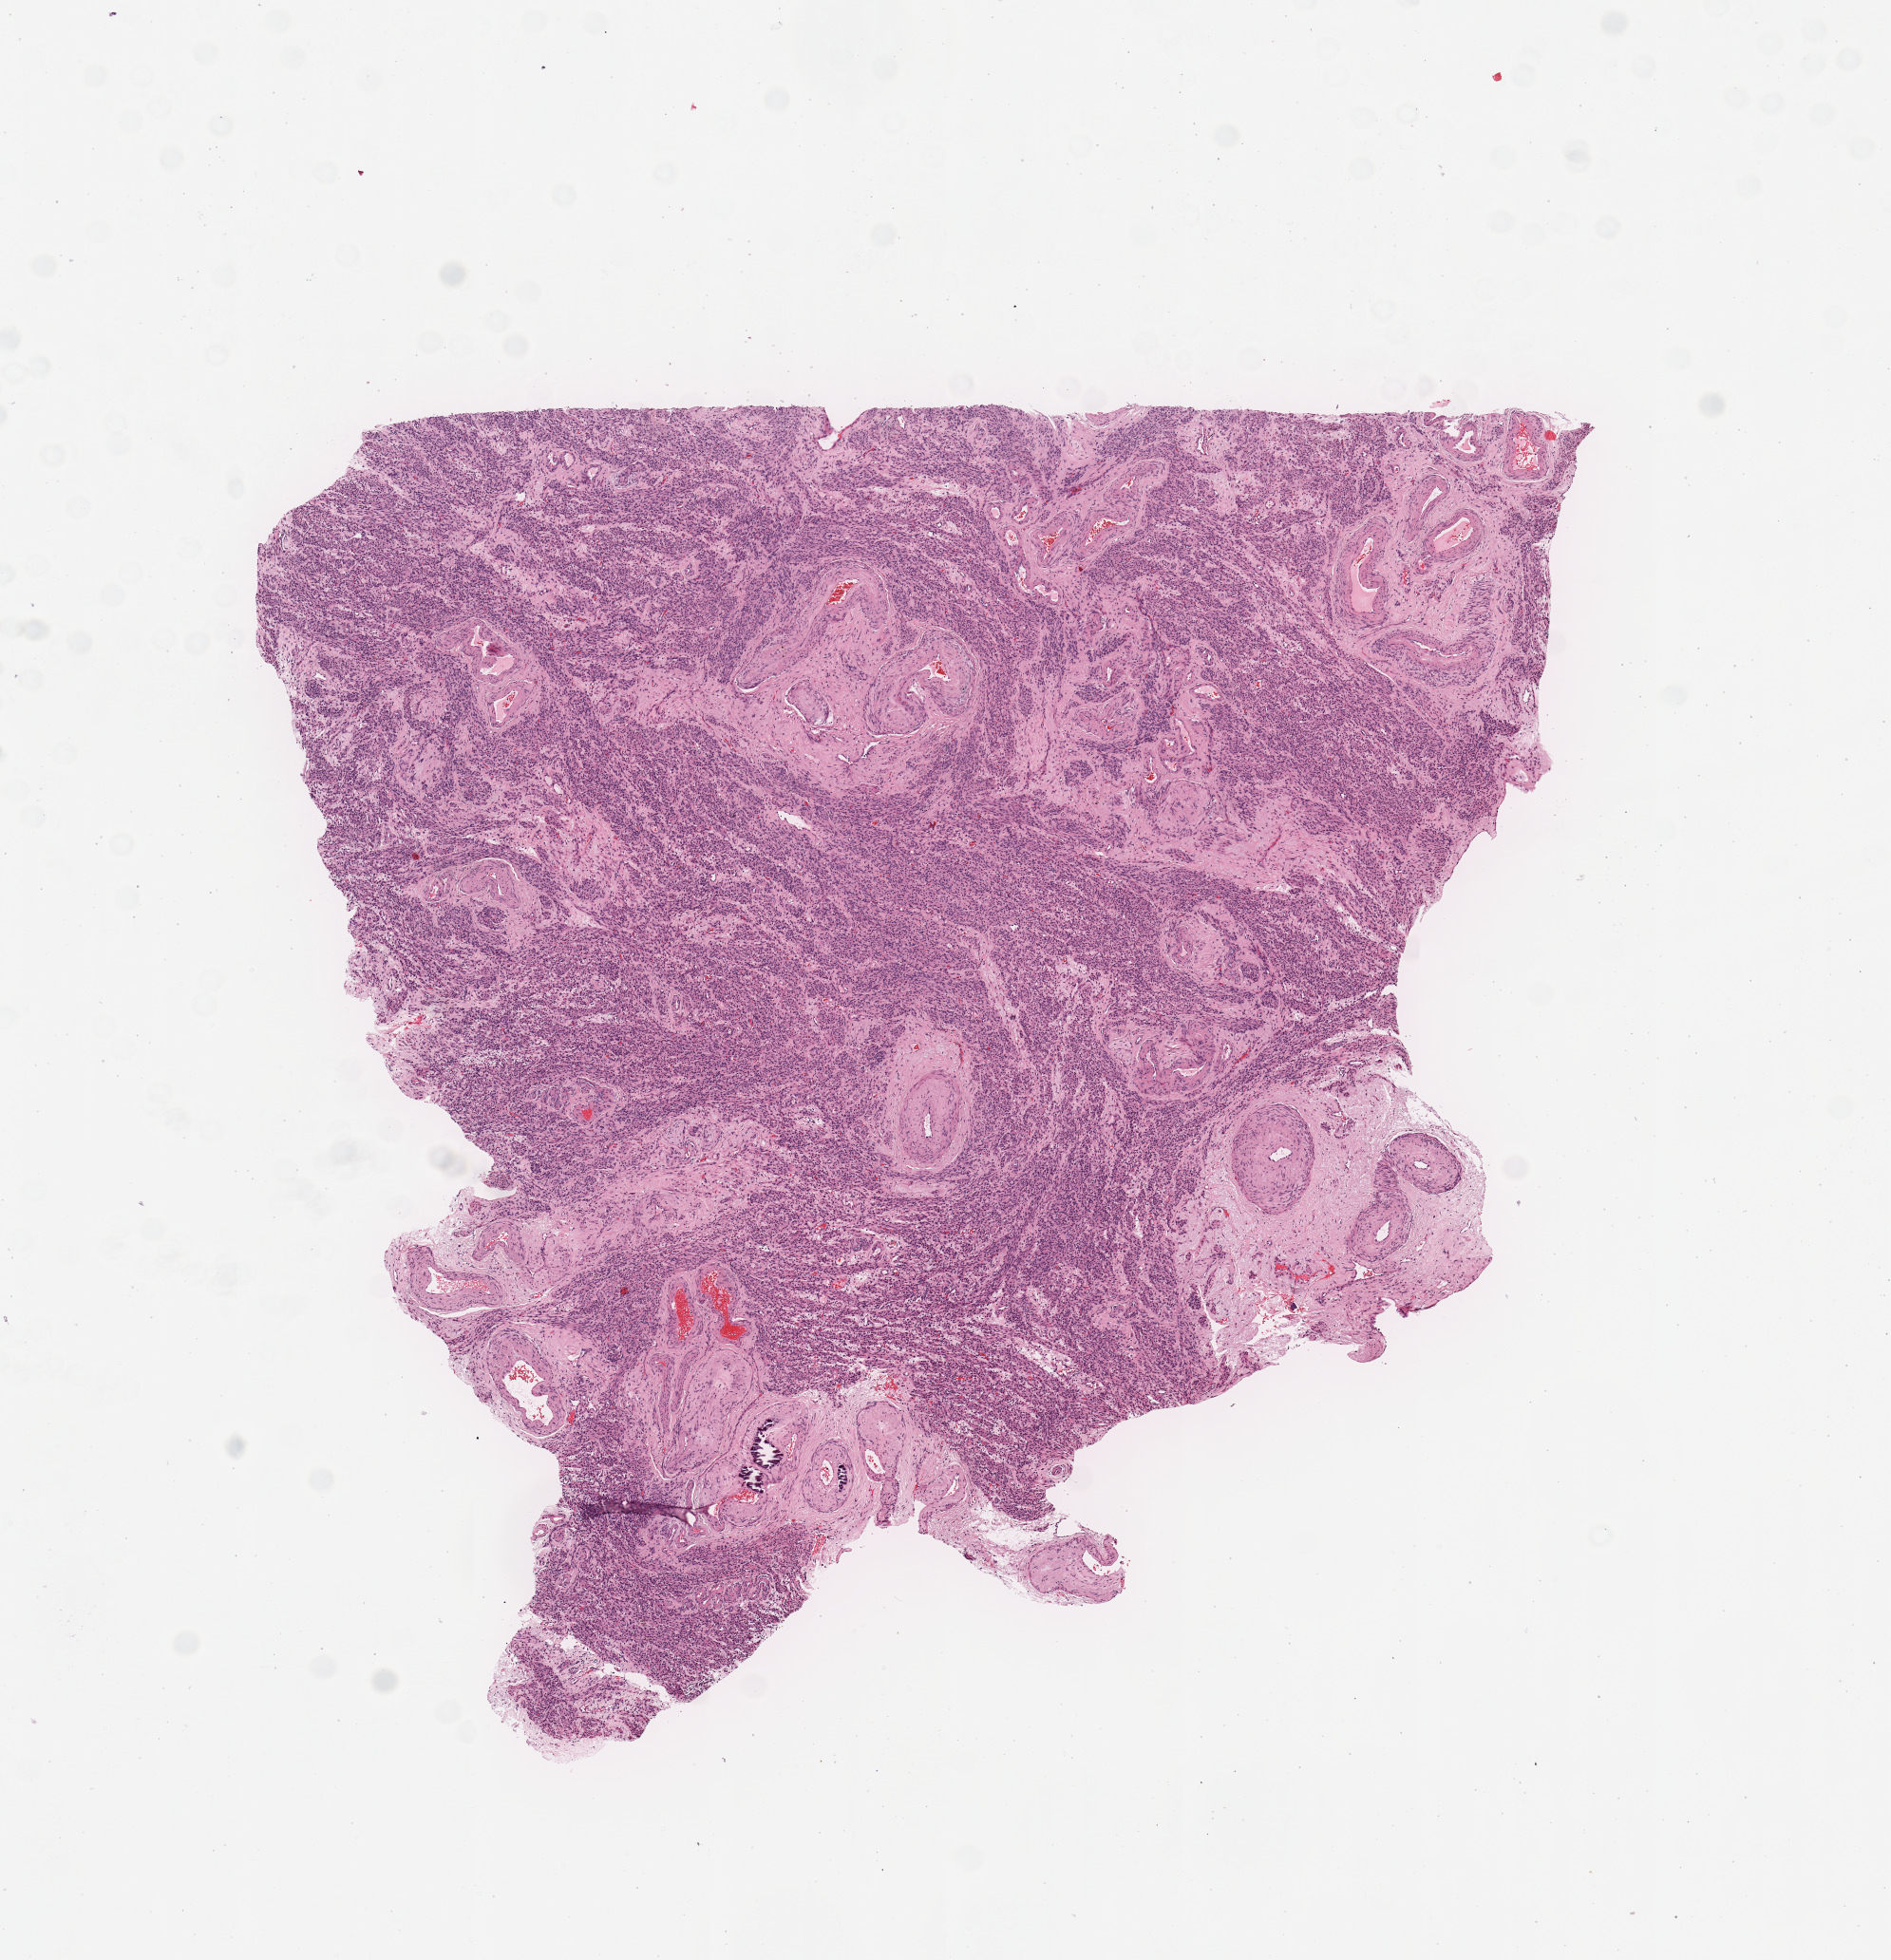
Whole-slide histology image, H&E-stained, whole scanned area (about 7.9 x 8.2 mm, acquisition: 20x scan) shown as a low-resolution overview. Uterus, normal (non-tumour) tissue. 83-year-old female patient.
- this section: normal (non-tumour) tissue from the same patient
- patient diagnosis: Endometrioid adenocarcinoma, NOS